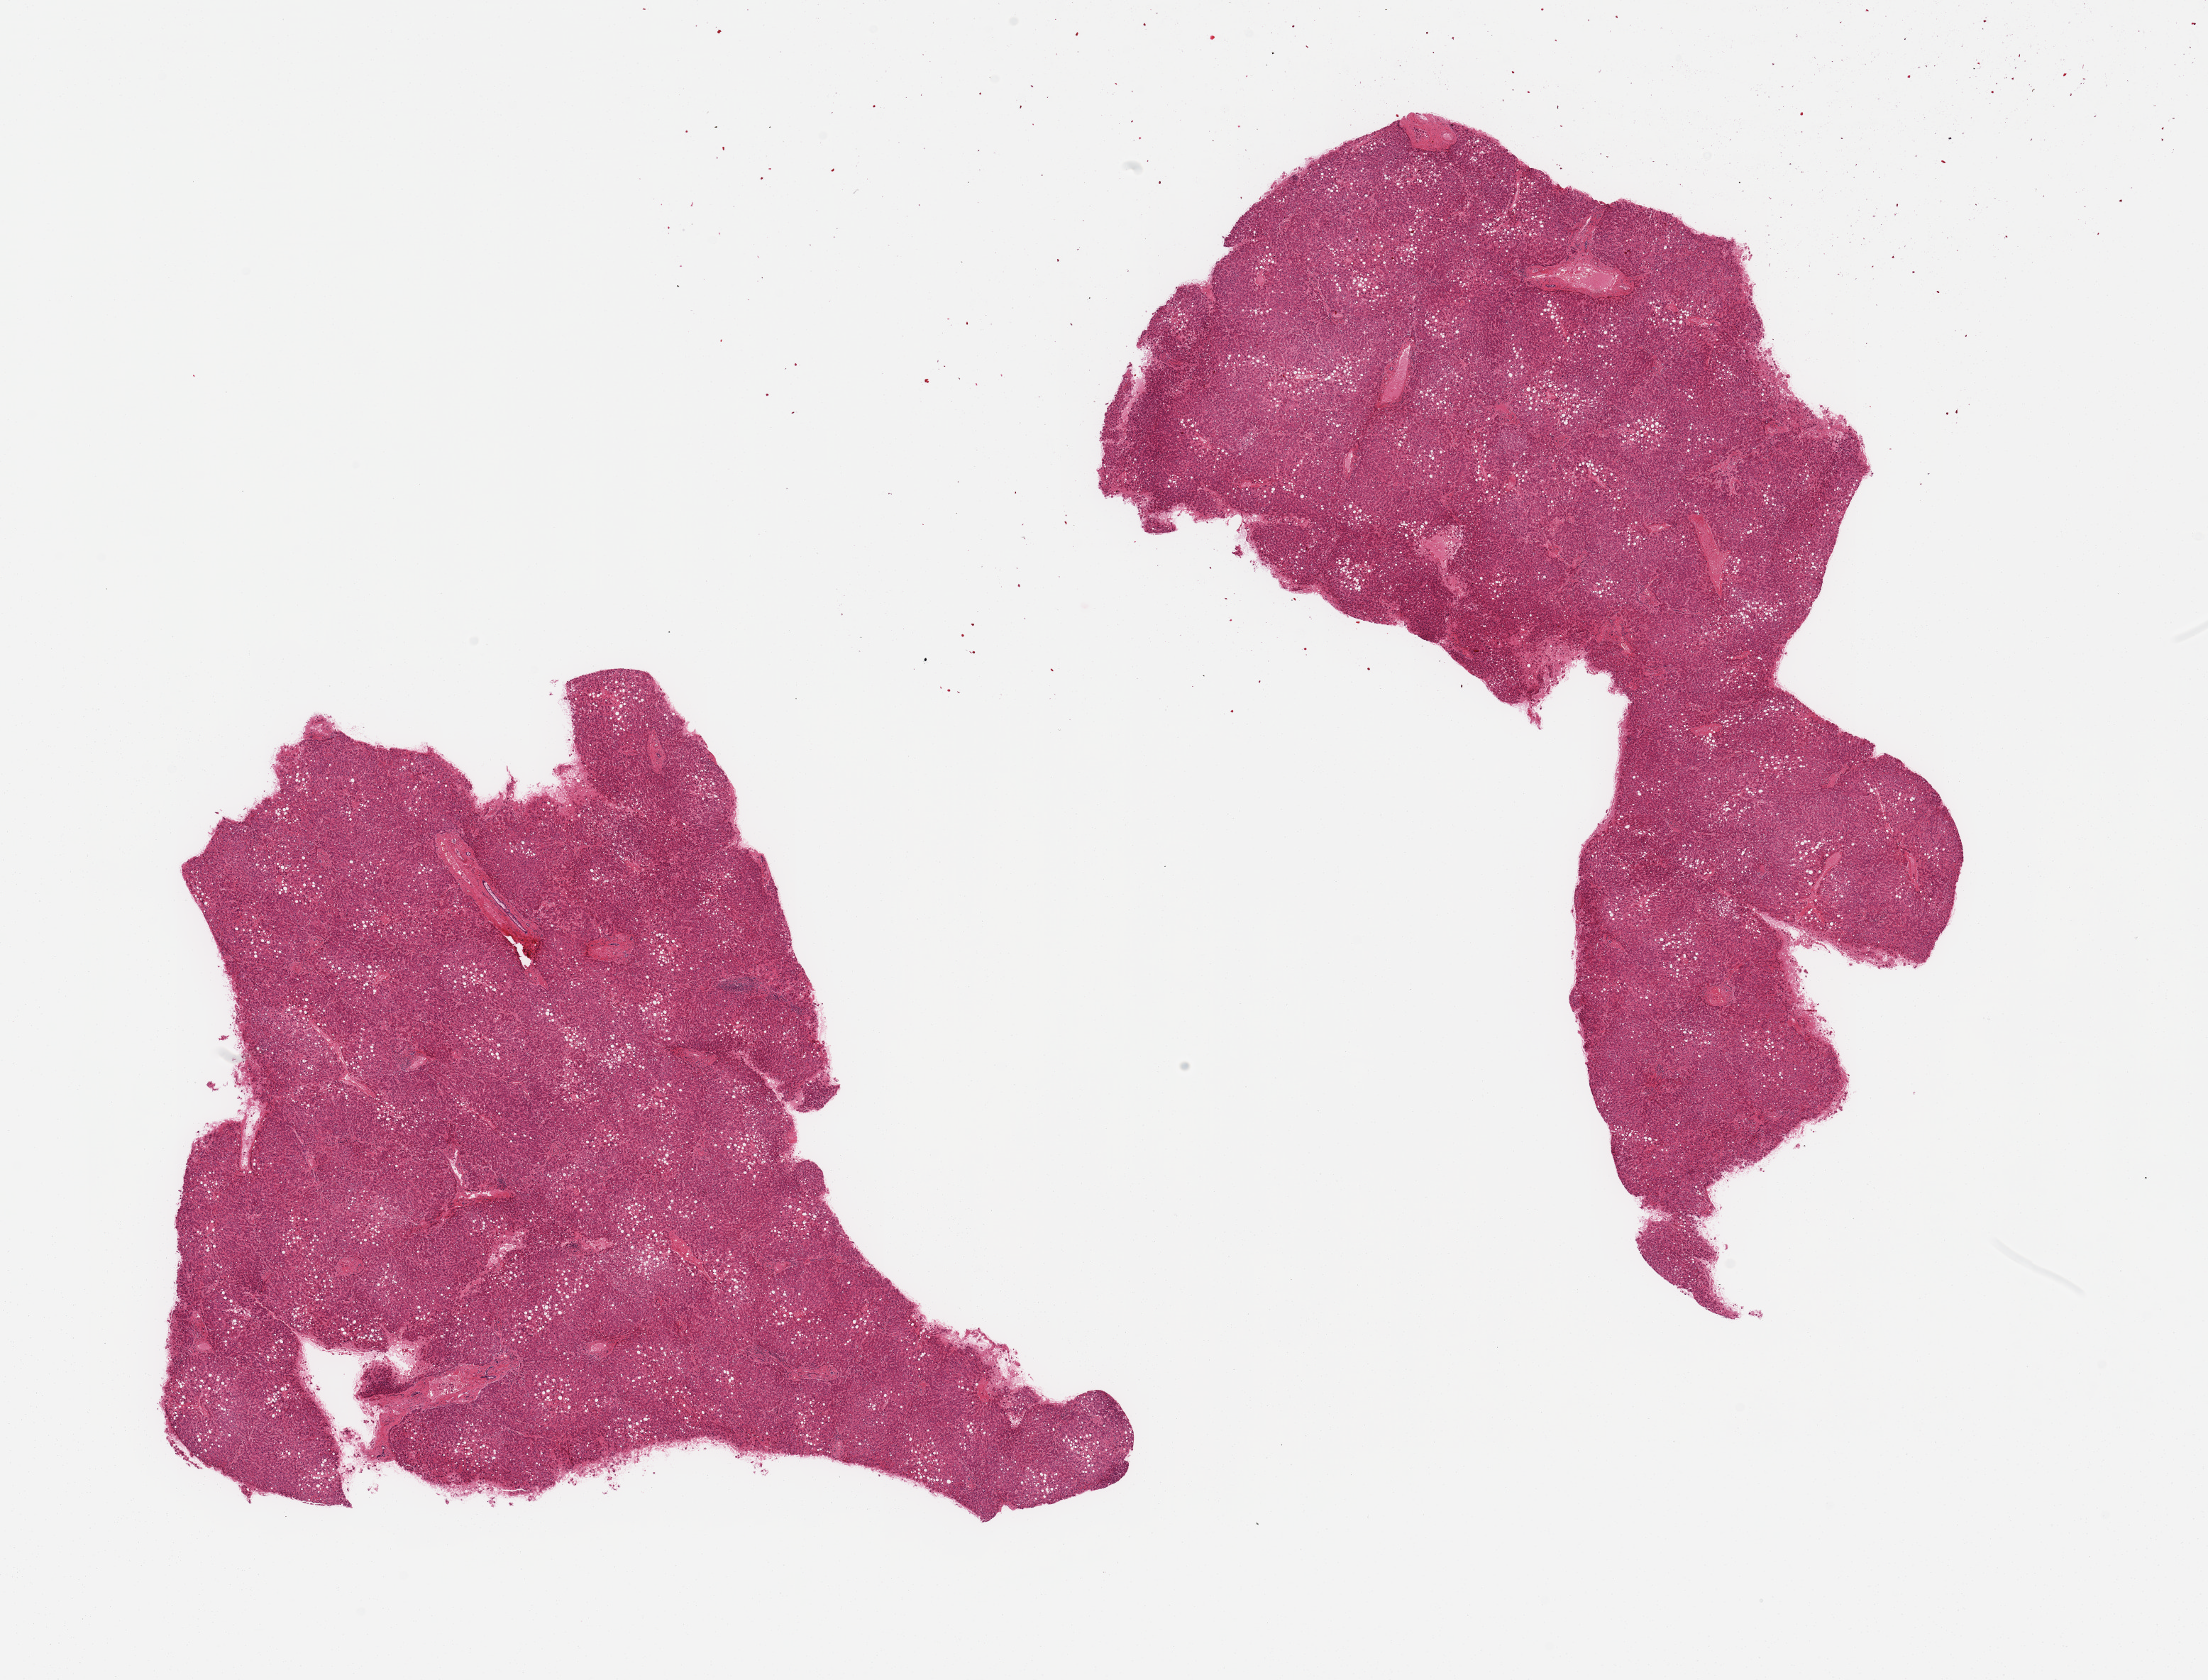
Hematoxylin and eosin (H&E) whole-slide image, brightfield, low-resolution overview of the scanned area, about 24.6 x 18.7 mm, PAXgene-fixed, paraffin-embedded tissue, sampled site (target tissue): liver, donor tissue sample.
Review note (as recorded): 2 pieces; 20% macrovesicular steatosis.